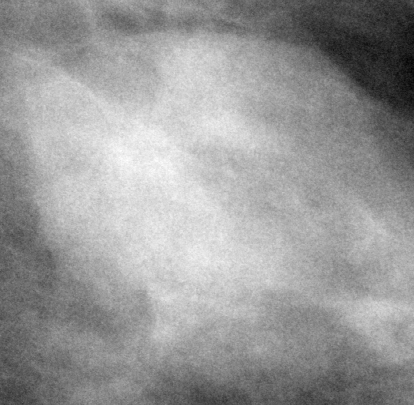
Cropped region of a digitized screen-film mammogram centred on a radiologist-marked abnormality; left breast; CC view; BI-RADS breast density category 2 (scale 1–4).
Mass, shape oval, margins circumscribed; BI-RADS assessment category 3; subtlety rating 5 on a 1 (subtle) to 5 (obvious) scale; pathology (as recorded): benign.